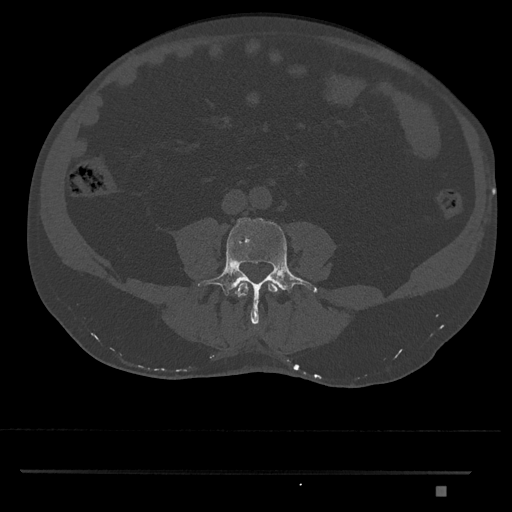
CT including the spine, one axial slice; slice 629 of 1134 in the series (ordered by position); 120 kVp; bone window (W 1800 / L 400 HU); 0.5 mm slice thickness; 512 × 512 image matrix. Male patient, age 65 years. Case-level facts recorded for this patient, not image findings: primary cancer: prostate.
Outlined on this slice (semi-automatic segmentation, software-assisted and operator-edited):
- L3 vertebra: bounding box (x1, y1, x2, y2) in pixels: (235, 281, 278, 297)
- L4 vertebra: (198, 217, 317, 325)